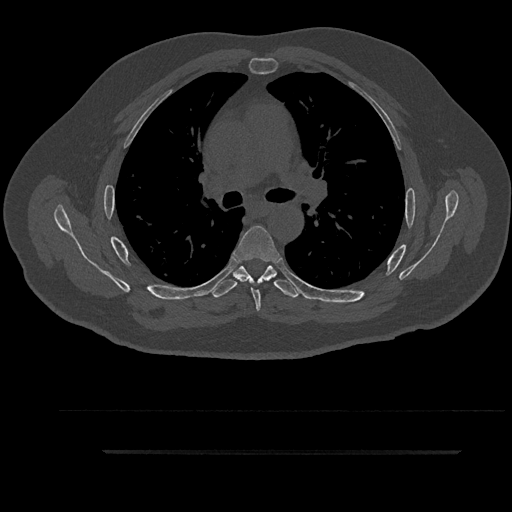
CT including the spine, one axial slice. Position 606 of 797 along the scan axis. 120 kVp. Bone window (W 1800 / L 400 HU). 512 × 512 image matrix, field of view 432 × 432 mm. Patient: male, 63 years. Case-level facts recorded for this patient, not image findings: primary cancer: renal; vertebrae with lytic lesions (as recorded): T8.
Structures marked on this image (semi-automatically segmented with operator editing):
- T5 vertebra: bounding box (x1, y1, x2, y2) in pixels: (233, 226, 281, 311)
- T6 vertebra: (211, 258, 301, 298)